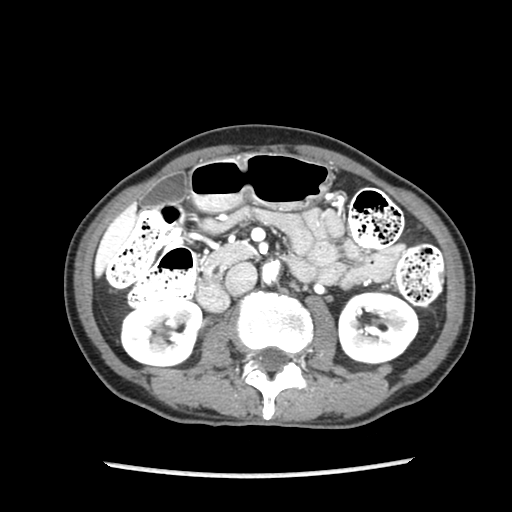
Contrast-enhanced abdominal CT (liver protocol), one axial slice; position 35 of 87 along the scan axis; 140 kVp; soft-tissue window (W 400 / L 40 HU); 2.5 mm slice thickness; 512 × 512 image matrix, field of view 300 × 300 mm. From the clinical record (not read from this slice): diagnosis: hepatocellular carcinoma (patient treated with transarterial chemoembolisation; whether this scan precedes or follows treatment is not stated here); TNM stage (as recorded): Stage-IIIB; Child-Pugh class: A.
Structures marked on this image (semi-automatically segmented with operator editing):
- liver parenchyma outside the tumour (the mass and vessels are separate outlines, so this box may not span the whole liver): box from (x=94, y=203) to (x=136, y=277) px
- liver vessels: (x=101, y=220)–(x=131, y=252)